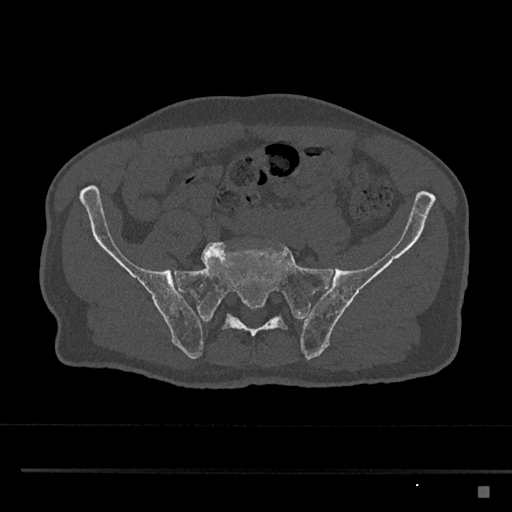
CT including the spine, one axial slice. Position 524 of 797 along the scan axis. 120 kVp. Bone window (W 1800 / L 400 HU). 0.5 mm slice thickness. 512 × 512 image matrix. Male patient, age 59 years. From the clinical record (not read from this slice): primary cancer: prostate.
Annotated regions visible in this slice (semi-automatically segmented with operator editing):
- L5 vertebra: bounding box <201,241,268,265> (left, top, right, bottom; pixels)